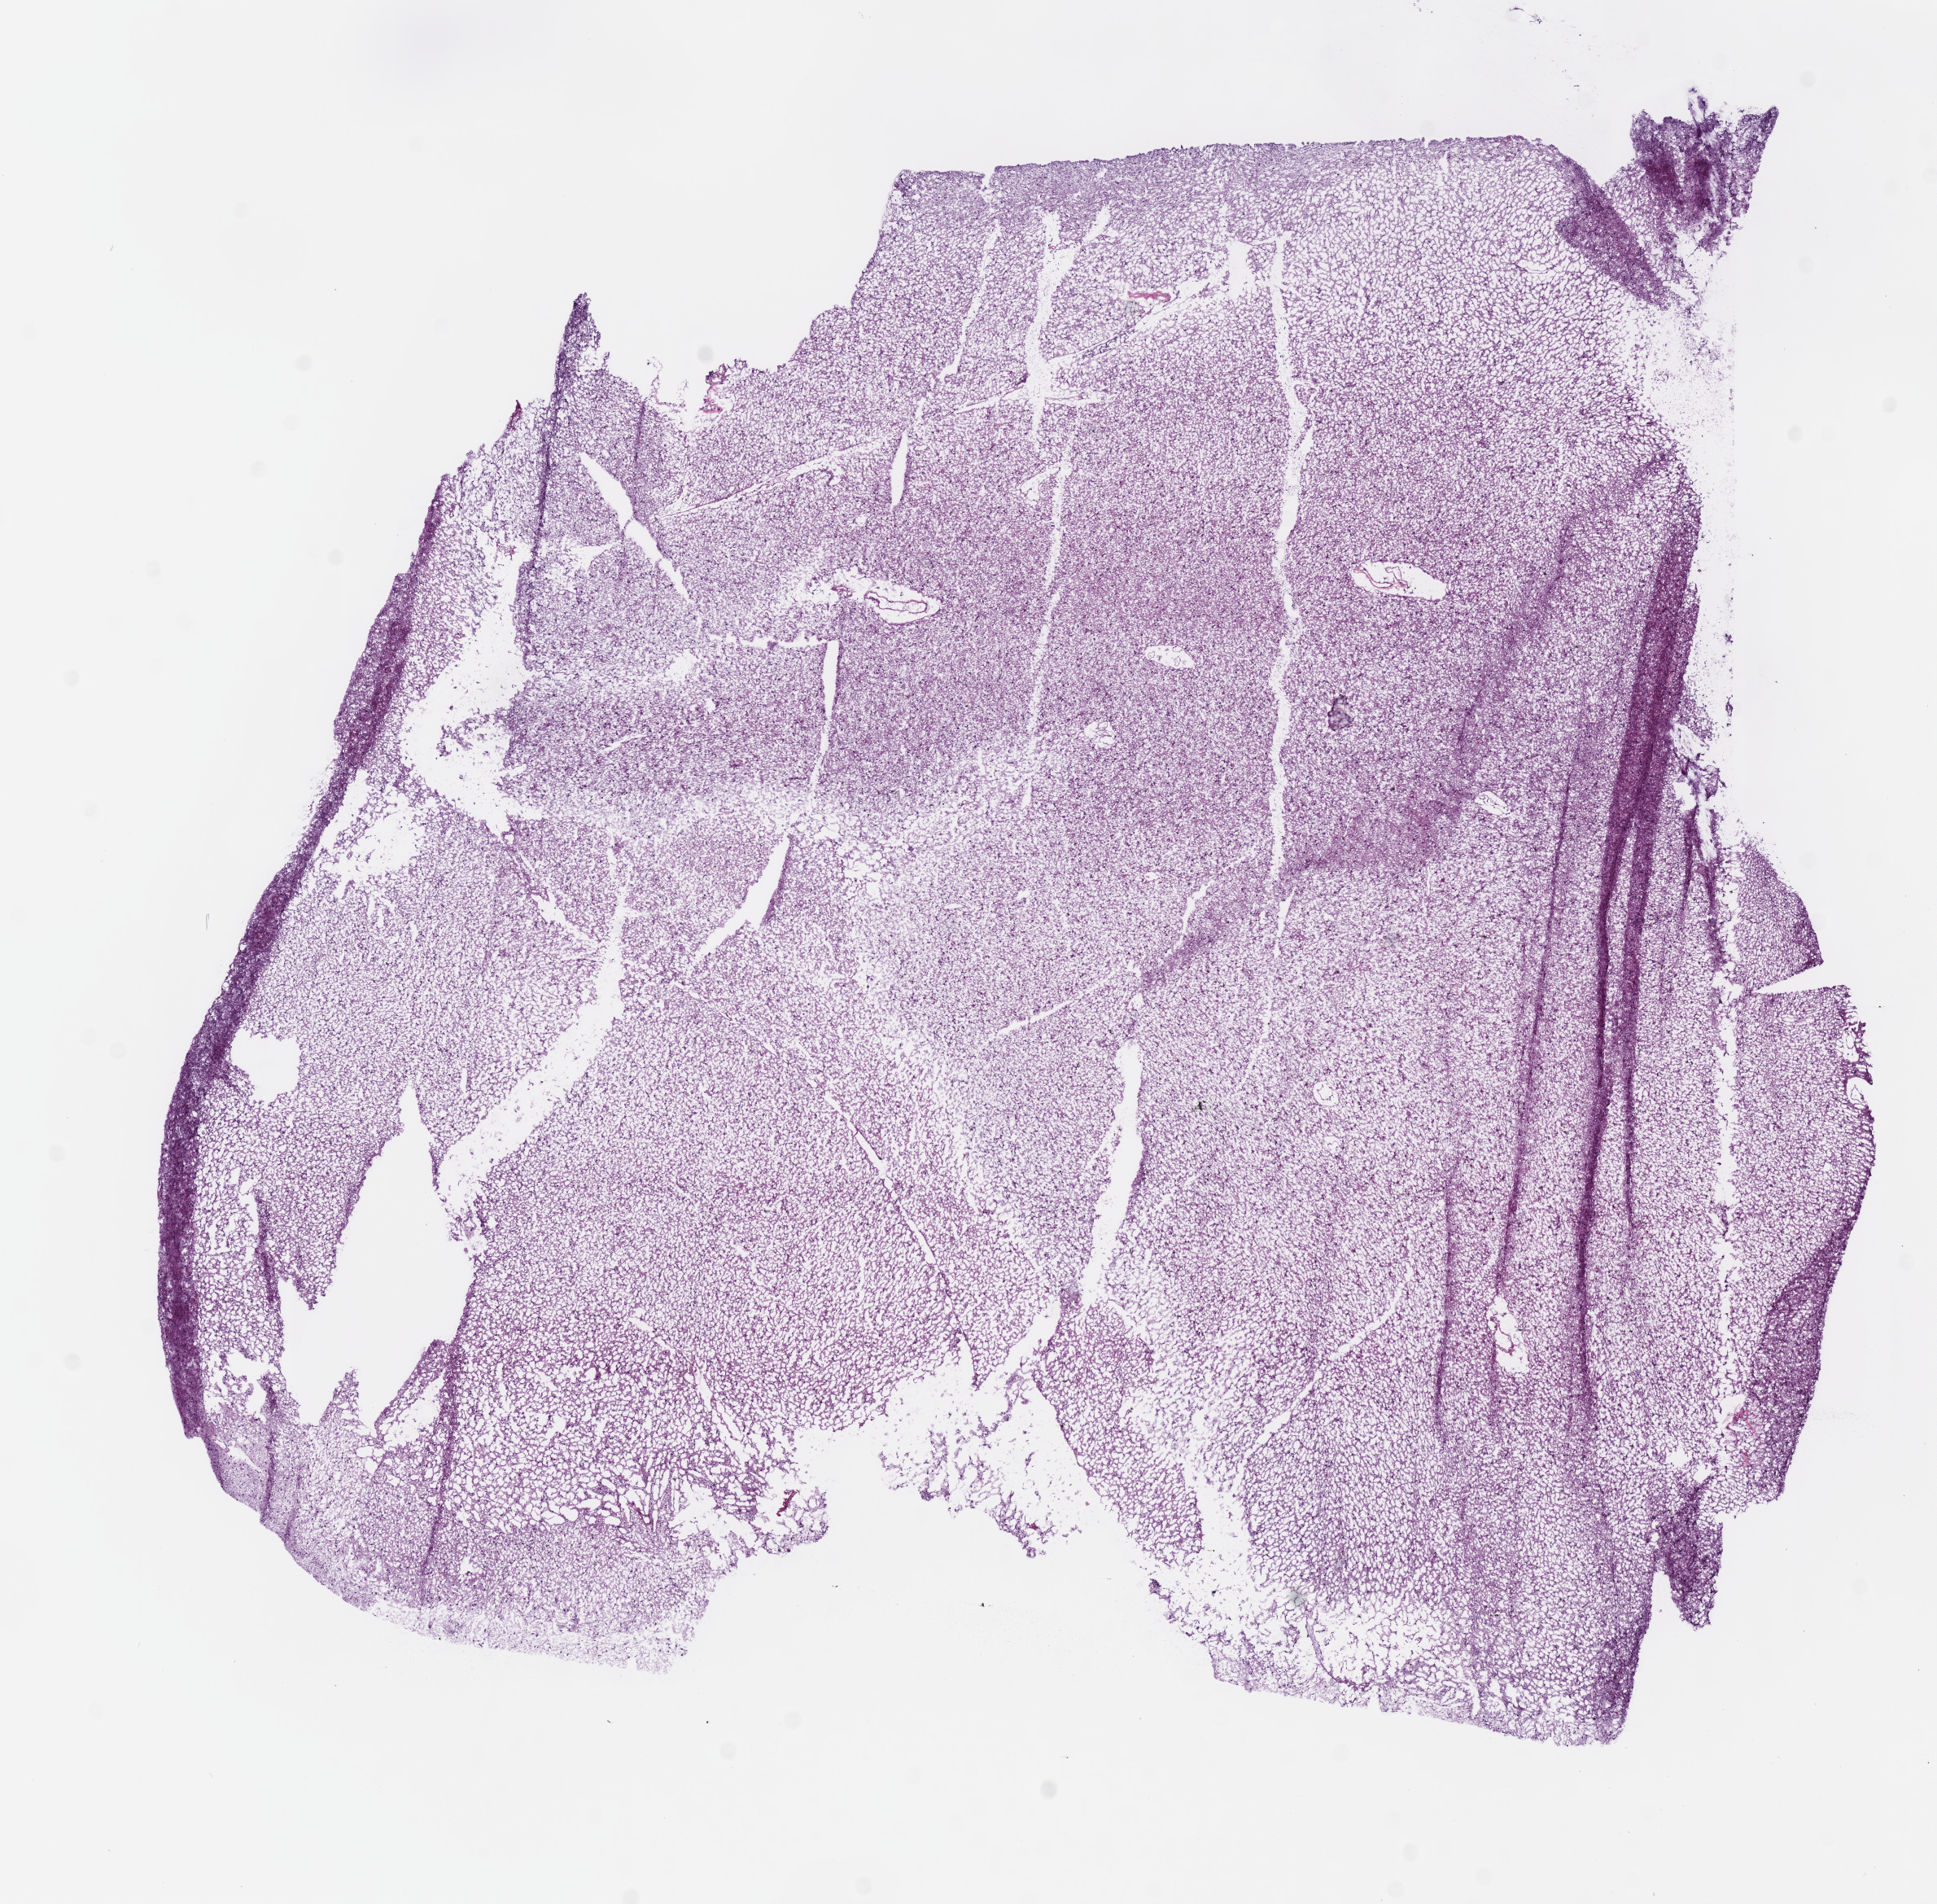
Whole-slide histology image, H&E-stained, shown as a low-resolution overview of the whole scanned area (about 9.4 x 9.2 mm); frozen section; brain, primary tumour sample. Female, age 58 years at initial diagnosis. Histologic grade: G2 (moderately differentiated). Slide review estimates, as recorded: tumour cells 100%, tumour nuclei 70%, normal cells 0%, stromal cells 0%, necrosis 0%.
Laterality: left. Pathologic diagnosis: Oligodendroglioma, NOS.